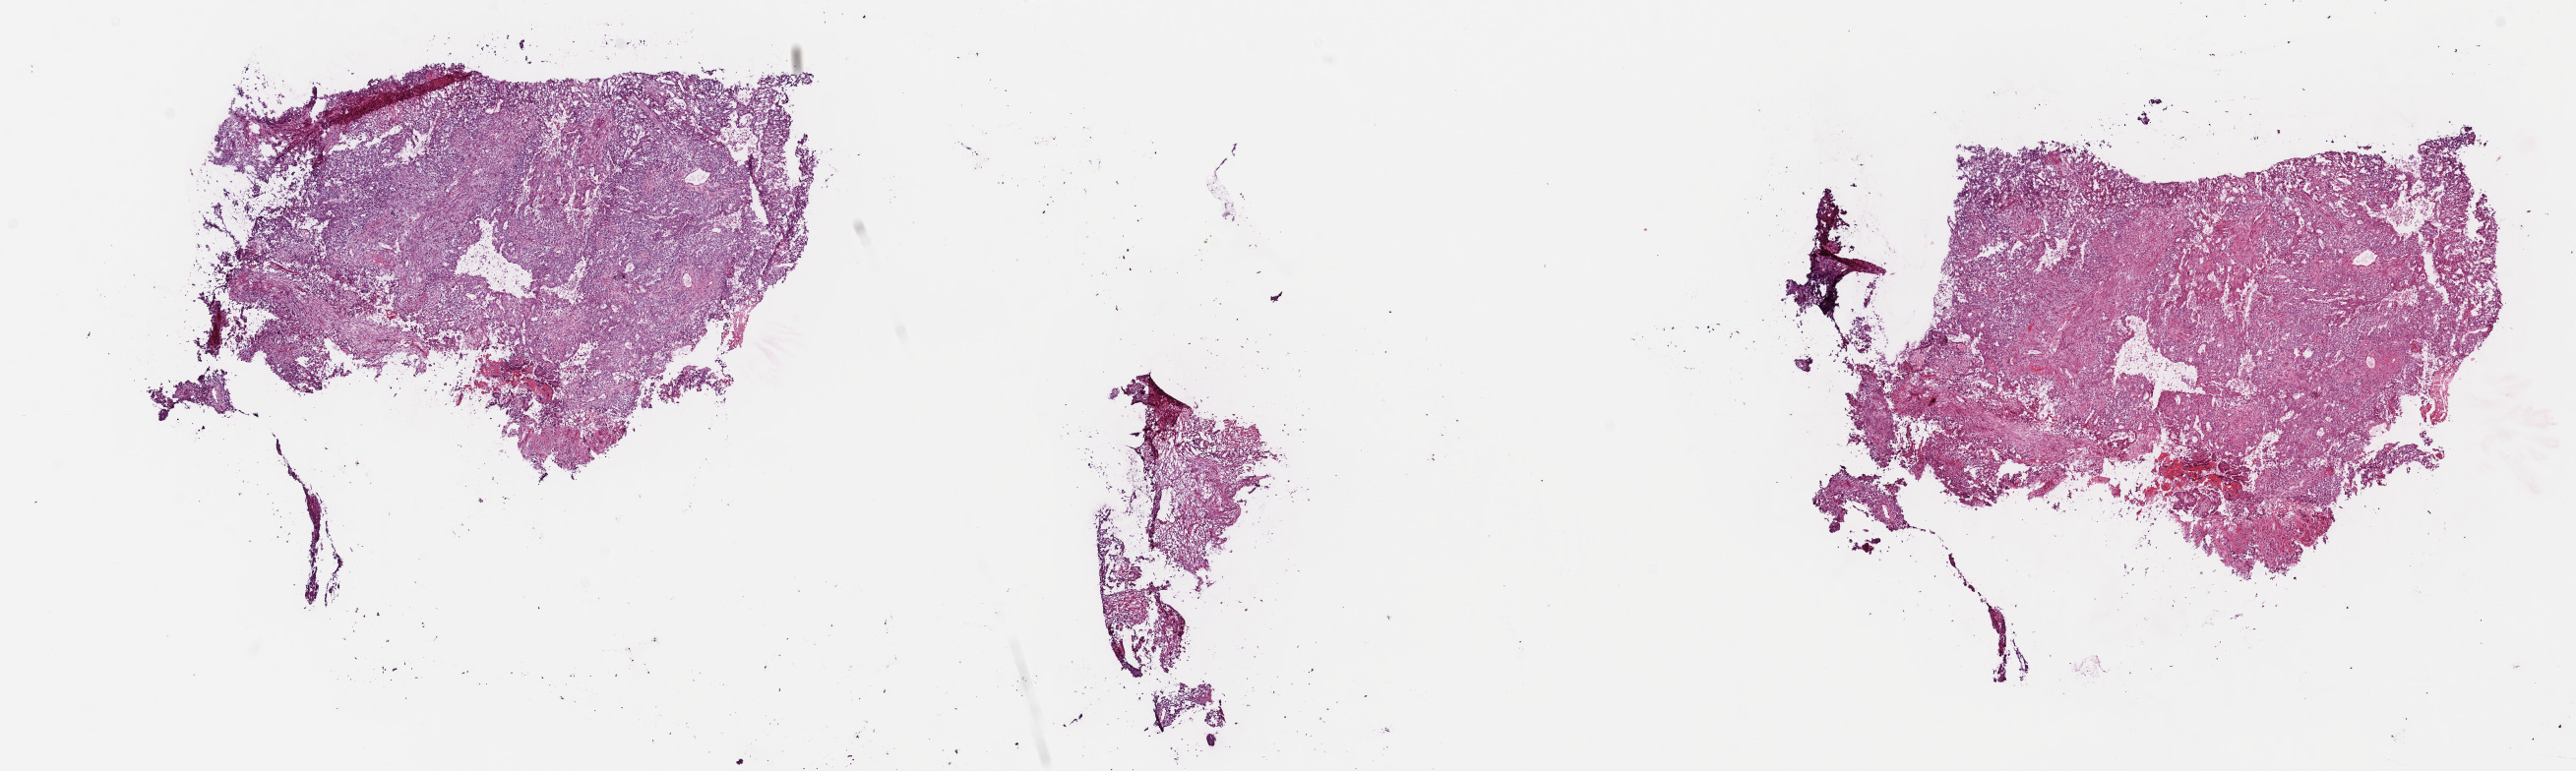
Hematoxylin and eosin (H&E) stained whole-slide image — shown as a low-resolution overview of the whole scanned area (about 20.7 x 6.2 mm, from a 40x scan), frozen section, uterus, primary tumour sample. Female, age 55 years at initial diagnosis. Histologic grade: G3 (poorly differentiated). Pathologist review of this section (percent, as recorded): tumour cells 70%, tumour nuclei 70%, normal cells 0%, stromal cells 20%, necrosis 10%. Infiltration values recorded for this section: lymphocyte infiltration 40%, monocyte infiltration 20%, neutrophil infiltration 20%.
FIGO stage: IA. Diagnosis: Endometrioid adenocarcinoma, NOS (endometrium).